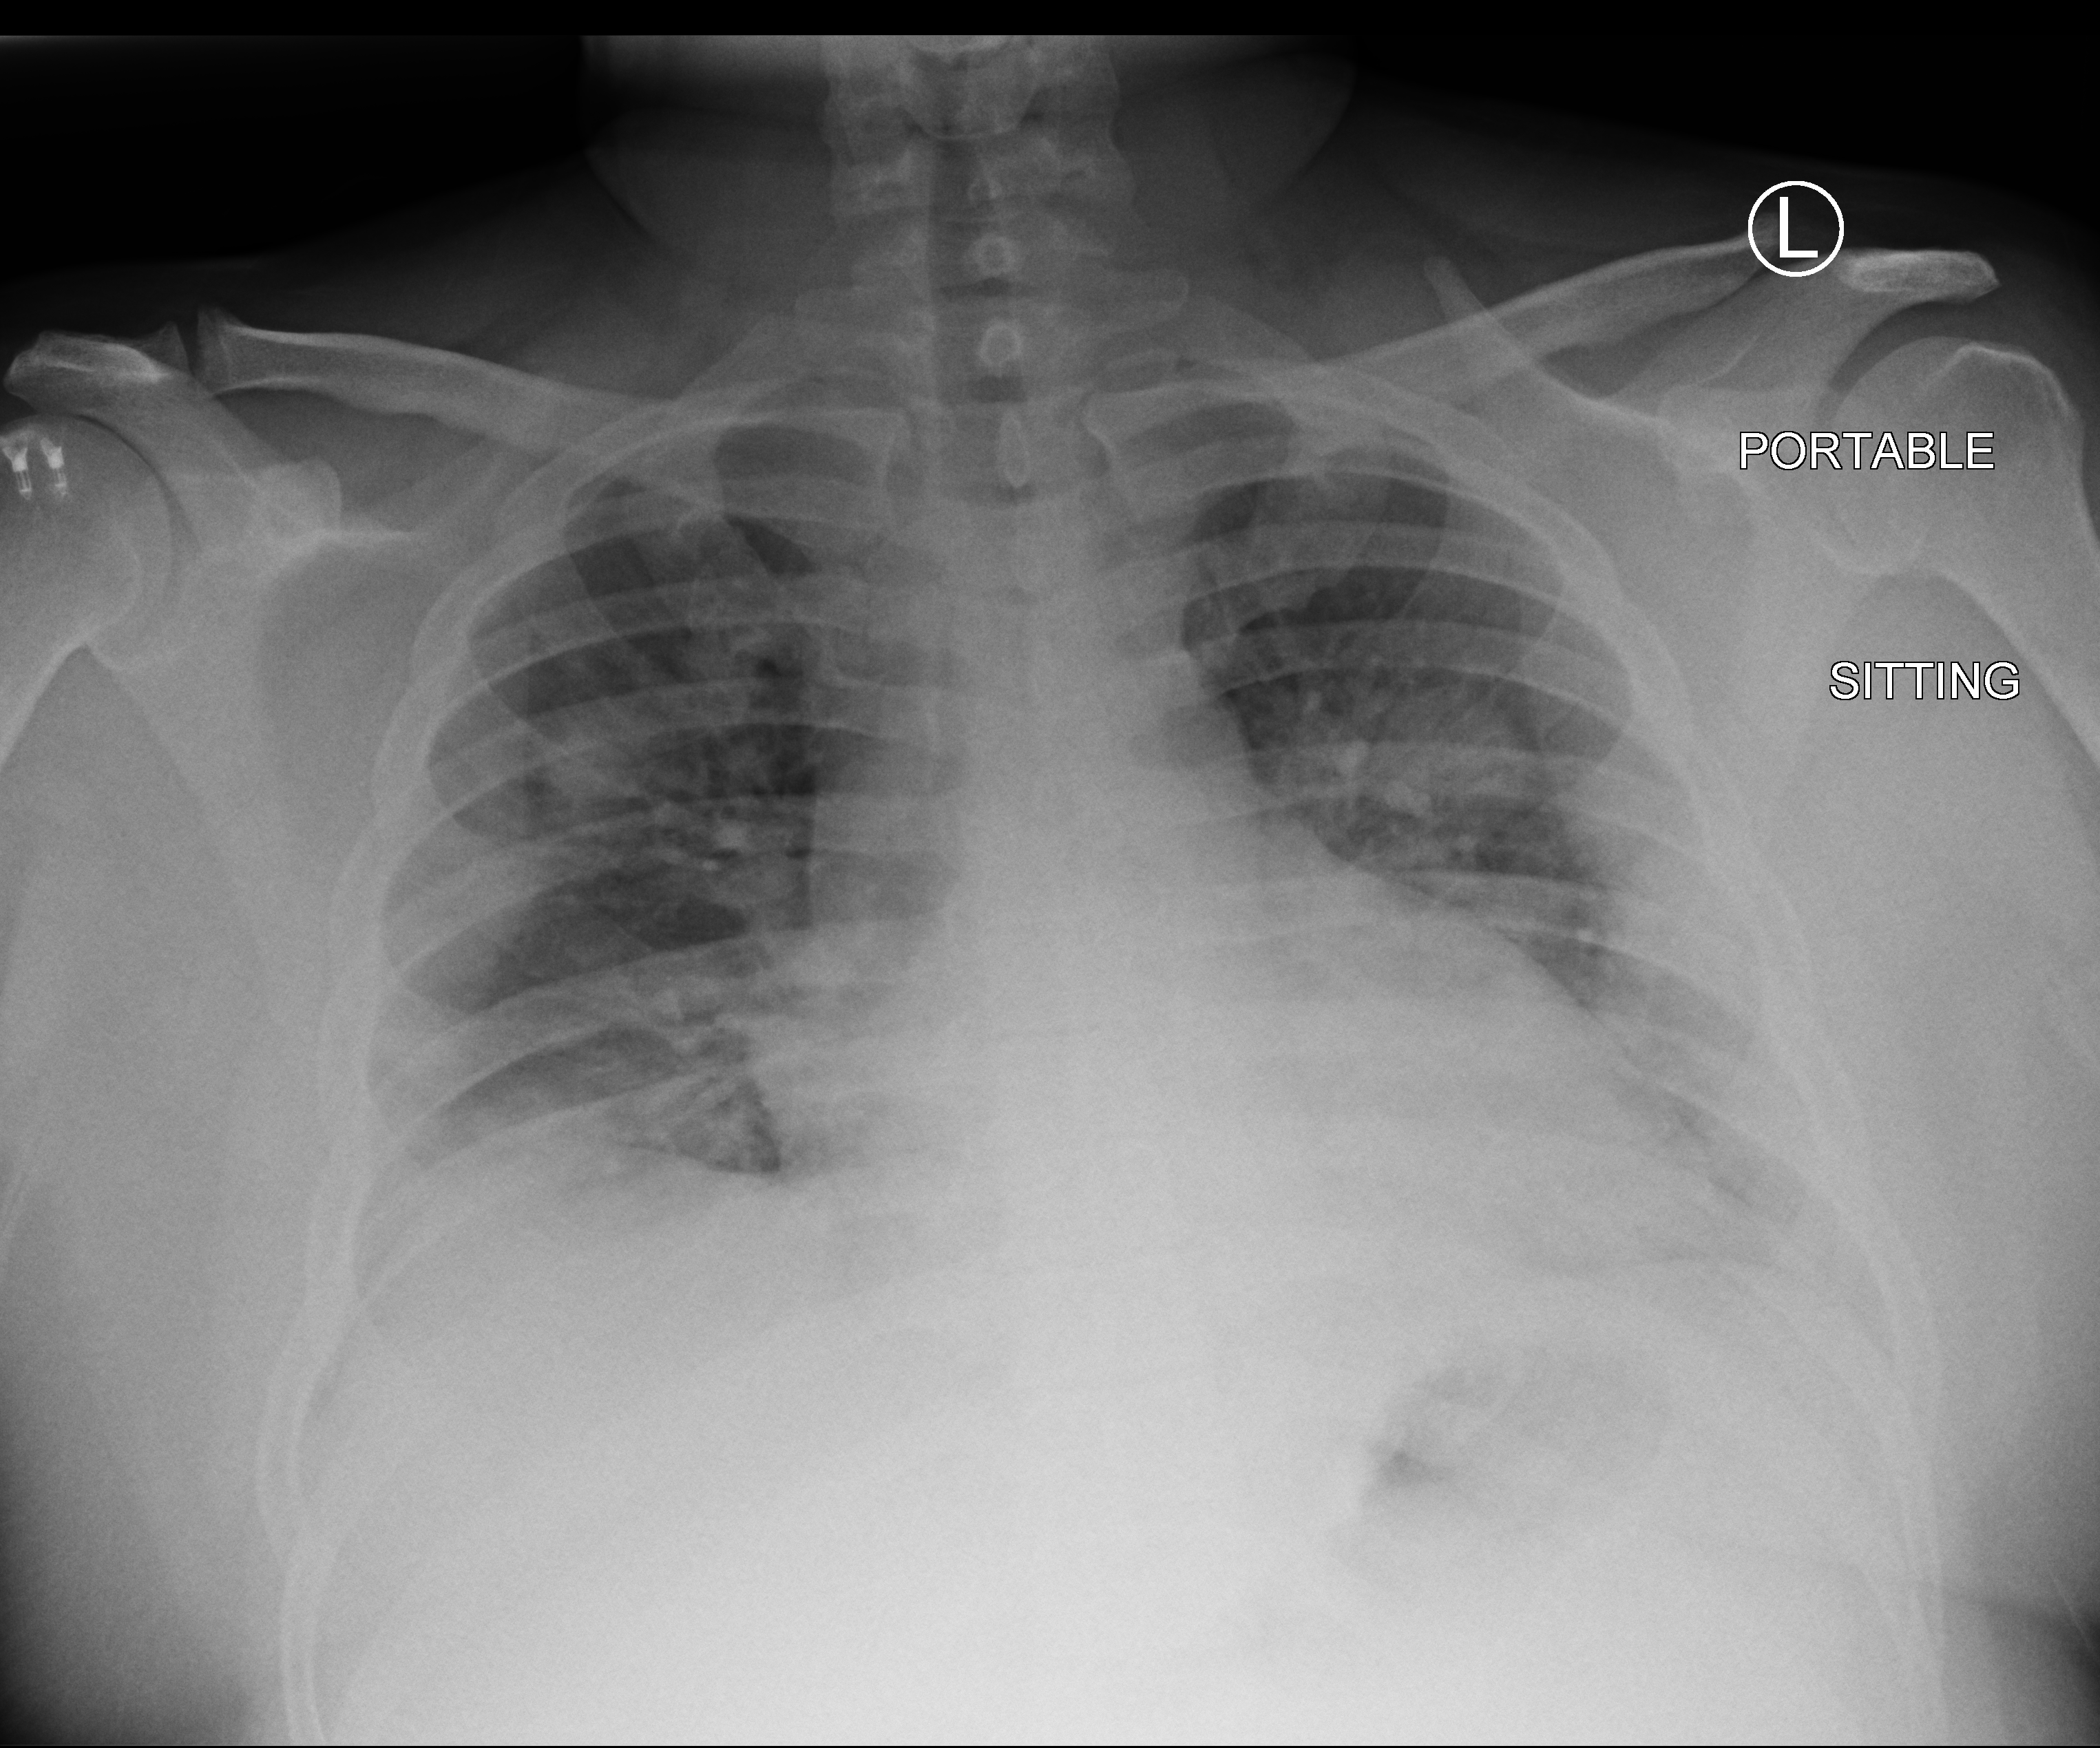
Portable chest radiograph, anteroposterior (AP) projection. Patient hospitalised with COVID-19; male, aged 18–59 years.
From the hospital-stay record, not from the radiograph (when in the stay this image was taken is not recorded): admitted to intensive care during this hospital stay: no.